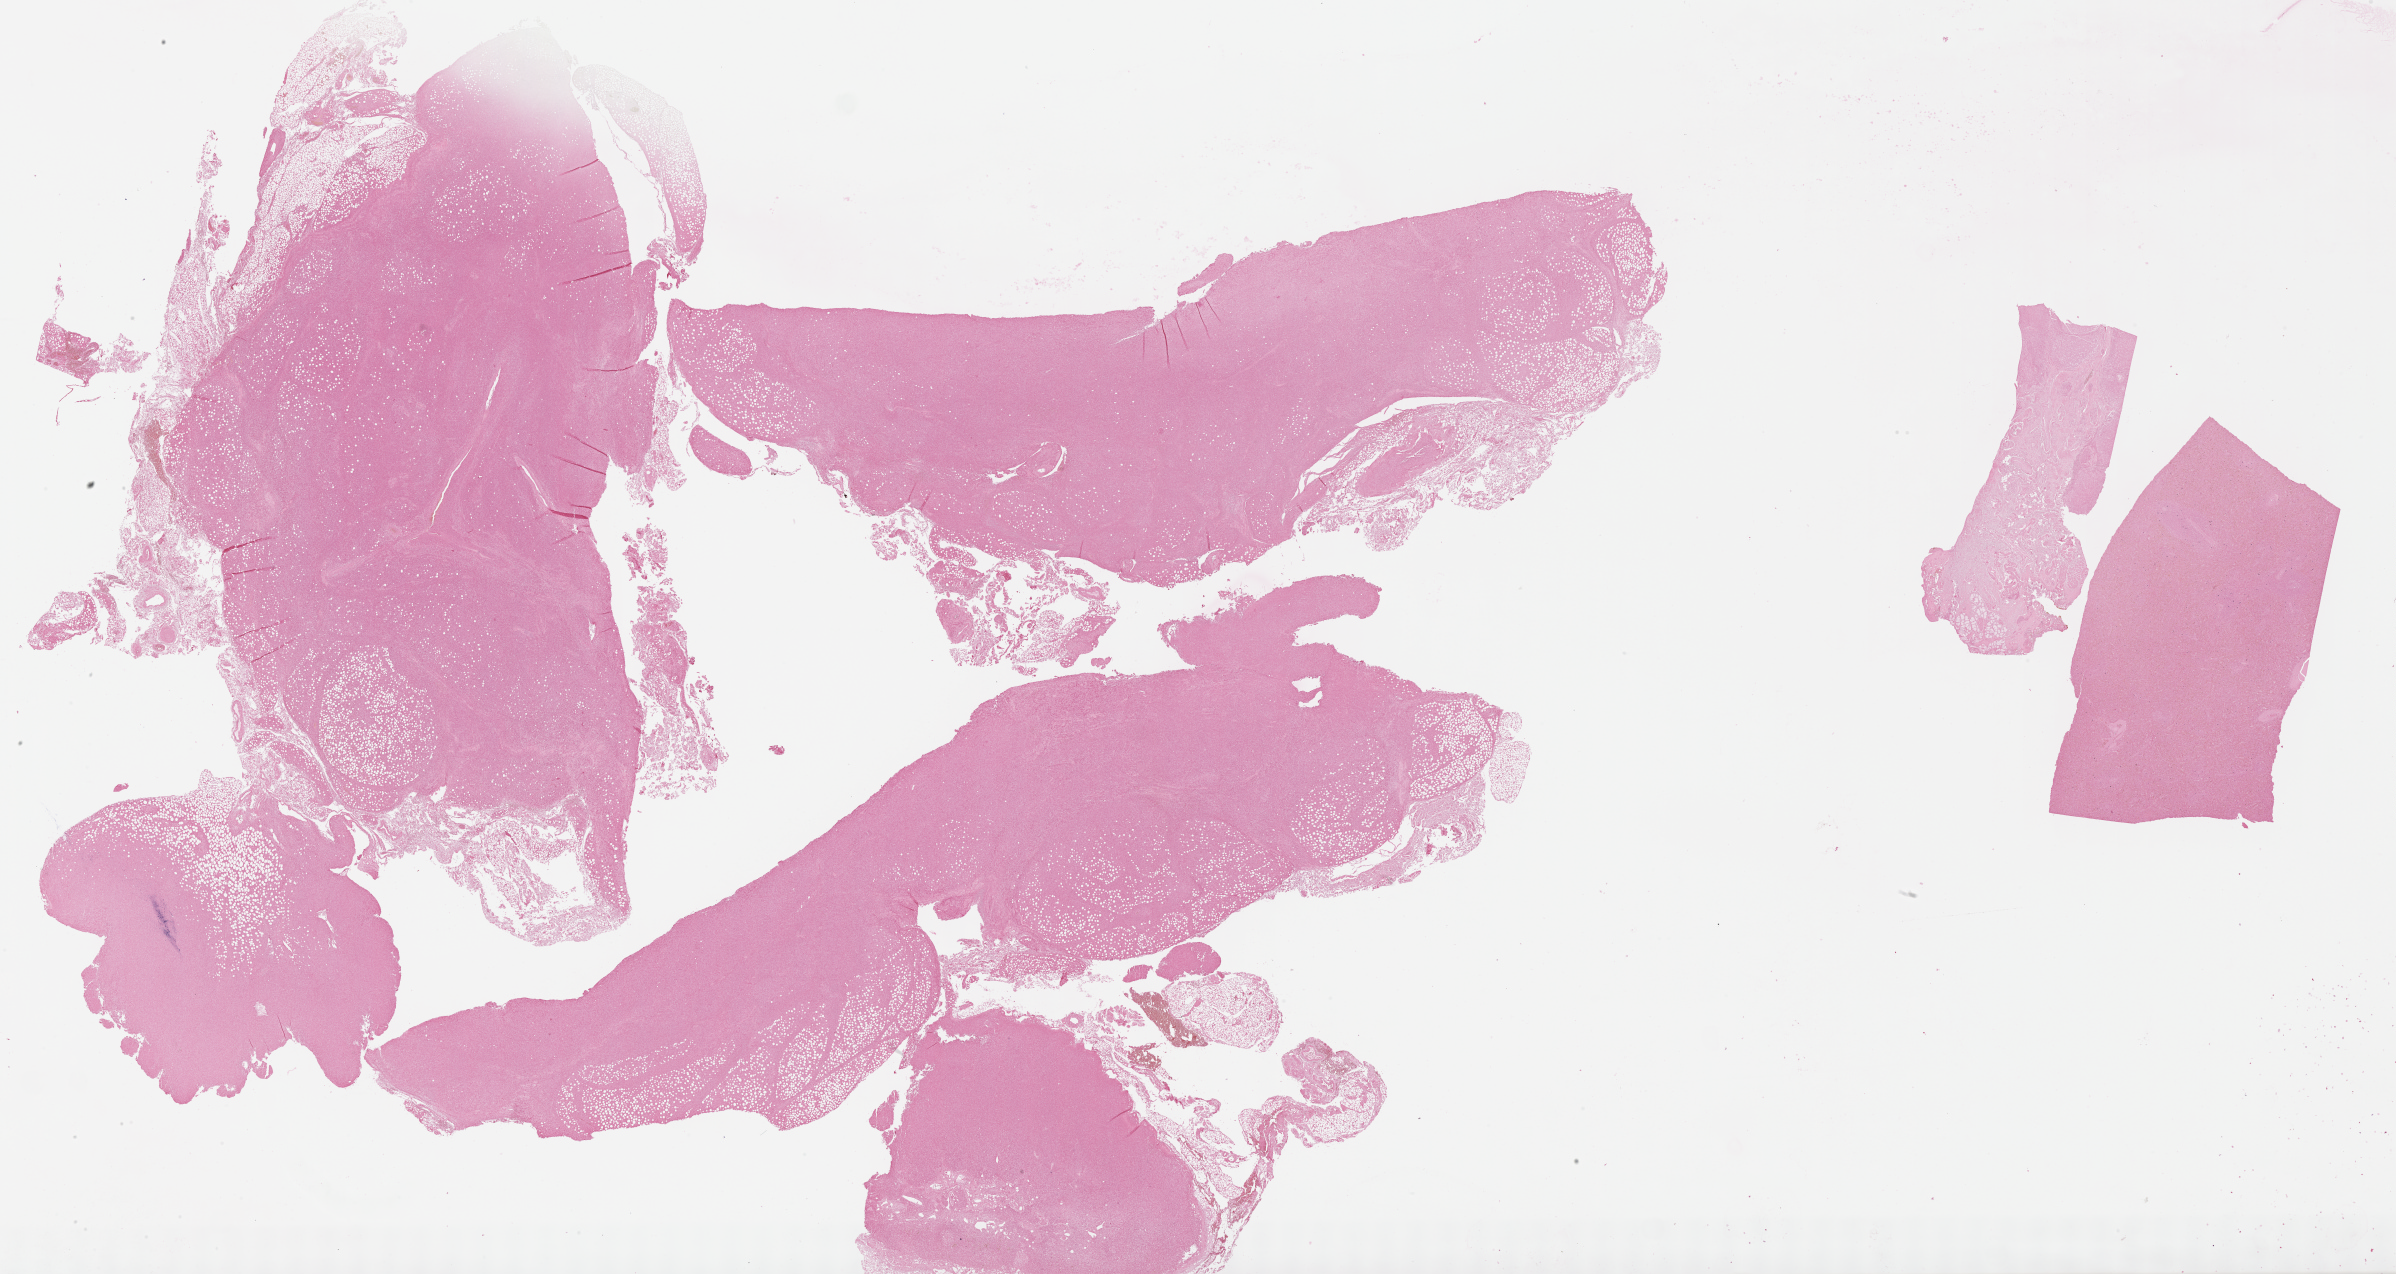
Whole-slide image, Epstein–Barr virus-encoded RNA (EBER) in-situ hybridisation, low-resolution overview of the scanned area, about 38.7 x 20.6 mm. Specimen: tumor tissue. Anatomic site: lymph node. Male patient, age 68 years.
Diagnosis: Diffuse large B-cell lymphoma, NOS.